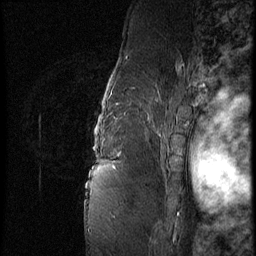
Breast MRI (dynamic contrast-enhanced), one sagittal slice; slice 59 of 62 in the series (ordered by position); 3 images stored at this slice position (order not interpretable as contrast timing); 1.5 T; TE 4.2 ms, TR 9 ms; 2.5 mm slice thickness; 256 × 256 image matrix. Patient: female, 56 years. Case-level facts recorded for this patient, not image findings: setting: breast cancer imaged before/during neoadjuvant chemotherapy; receptor status: HER2-positive.
Annotated regions visible in this slice (semi-automatically segmented with operator editing):
- analysis volume of interest (the breast-tissue region the enhancement analysis was run in; not a lesion): bounding box <84,75,181,153> (left, top, right, bottom; pixels)
- tumour enhancement mask (voxels above the 140 % enhancement threshold inside the analysis volume of interest): <104,85,120,153>